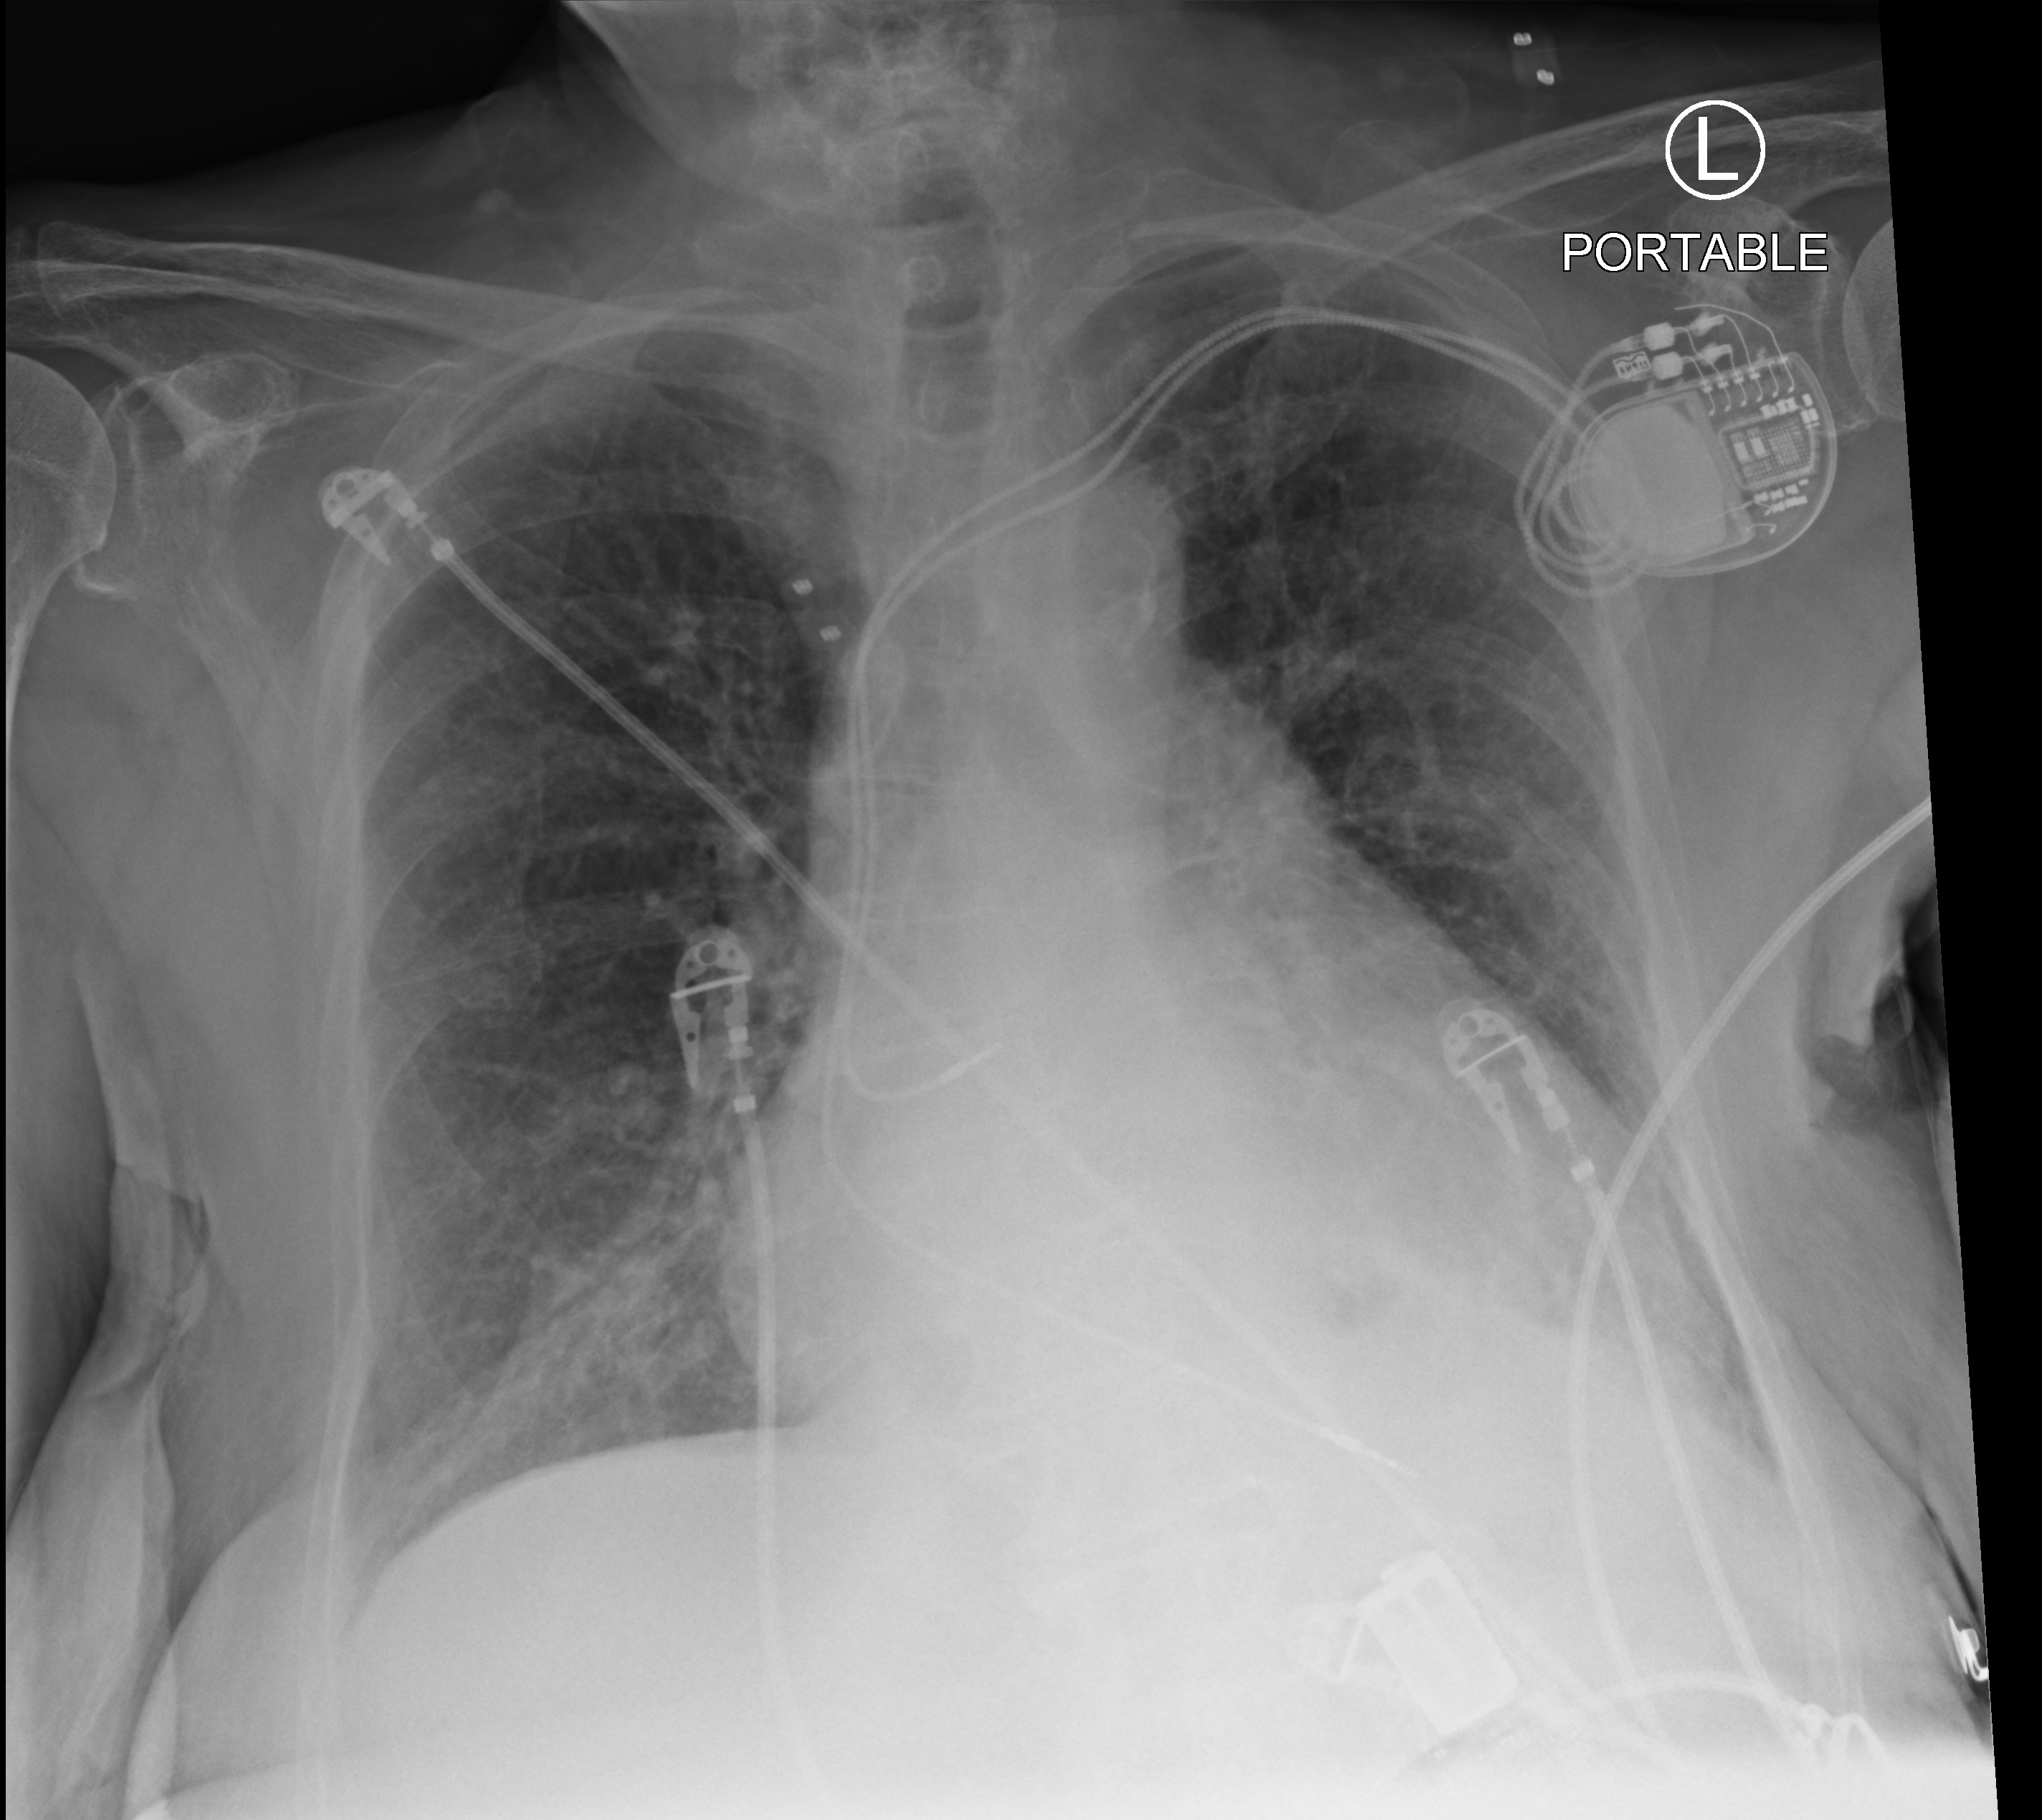
Bedside chest radiograph (computed radiography); anteroposterior (AP) projection. Patient hospitalised with COVID-19; female, aged 75–90 years.
Hospital-stay facts (about this admission, not read from this image; timing relative to this image not recorded): admitted to intensive care during this hospital stay: no.